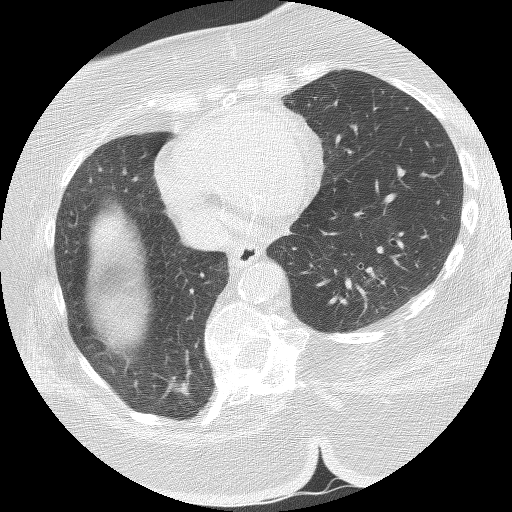
Chest CT (low-dose screening protocol), one axial image; baseline screening round; lung window (W 1500 / L -600 HU); lung (sharp) reconstruction kernel (BONE); 140 kVp; slice 99 of 151 in the series; 512 × 512 image matrix, field of view 340 × 340 mm. Female participant, aged 59 years at enrolment.
- Expert-annotated lung lesion, box from (x=145, y=344) to (x=203, y=413) px.
- Reader record for this screening exam (exam-level; its link to the box is not recorded): non-calcified nodule or mass ≥4 mm, right lower lobe, 21 × 10 mm, spiculated (stellate) margins, soft tissue attenuation.
- Official screen result: positive, change unspecified: nodule(s) >= 4 mm or enlarging nodule(s), mass(es), or other non-specific abnormalities suspicious for lung cancer.
- Later outcome: lung cancer diagnosed 52 days after this screen — bronchiolo-alveolar carcinoma, mucinous, right lower lobe, well differentiated (G1), stage IA (AJCC 6th edition), 15 mm at pathology.